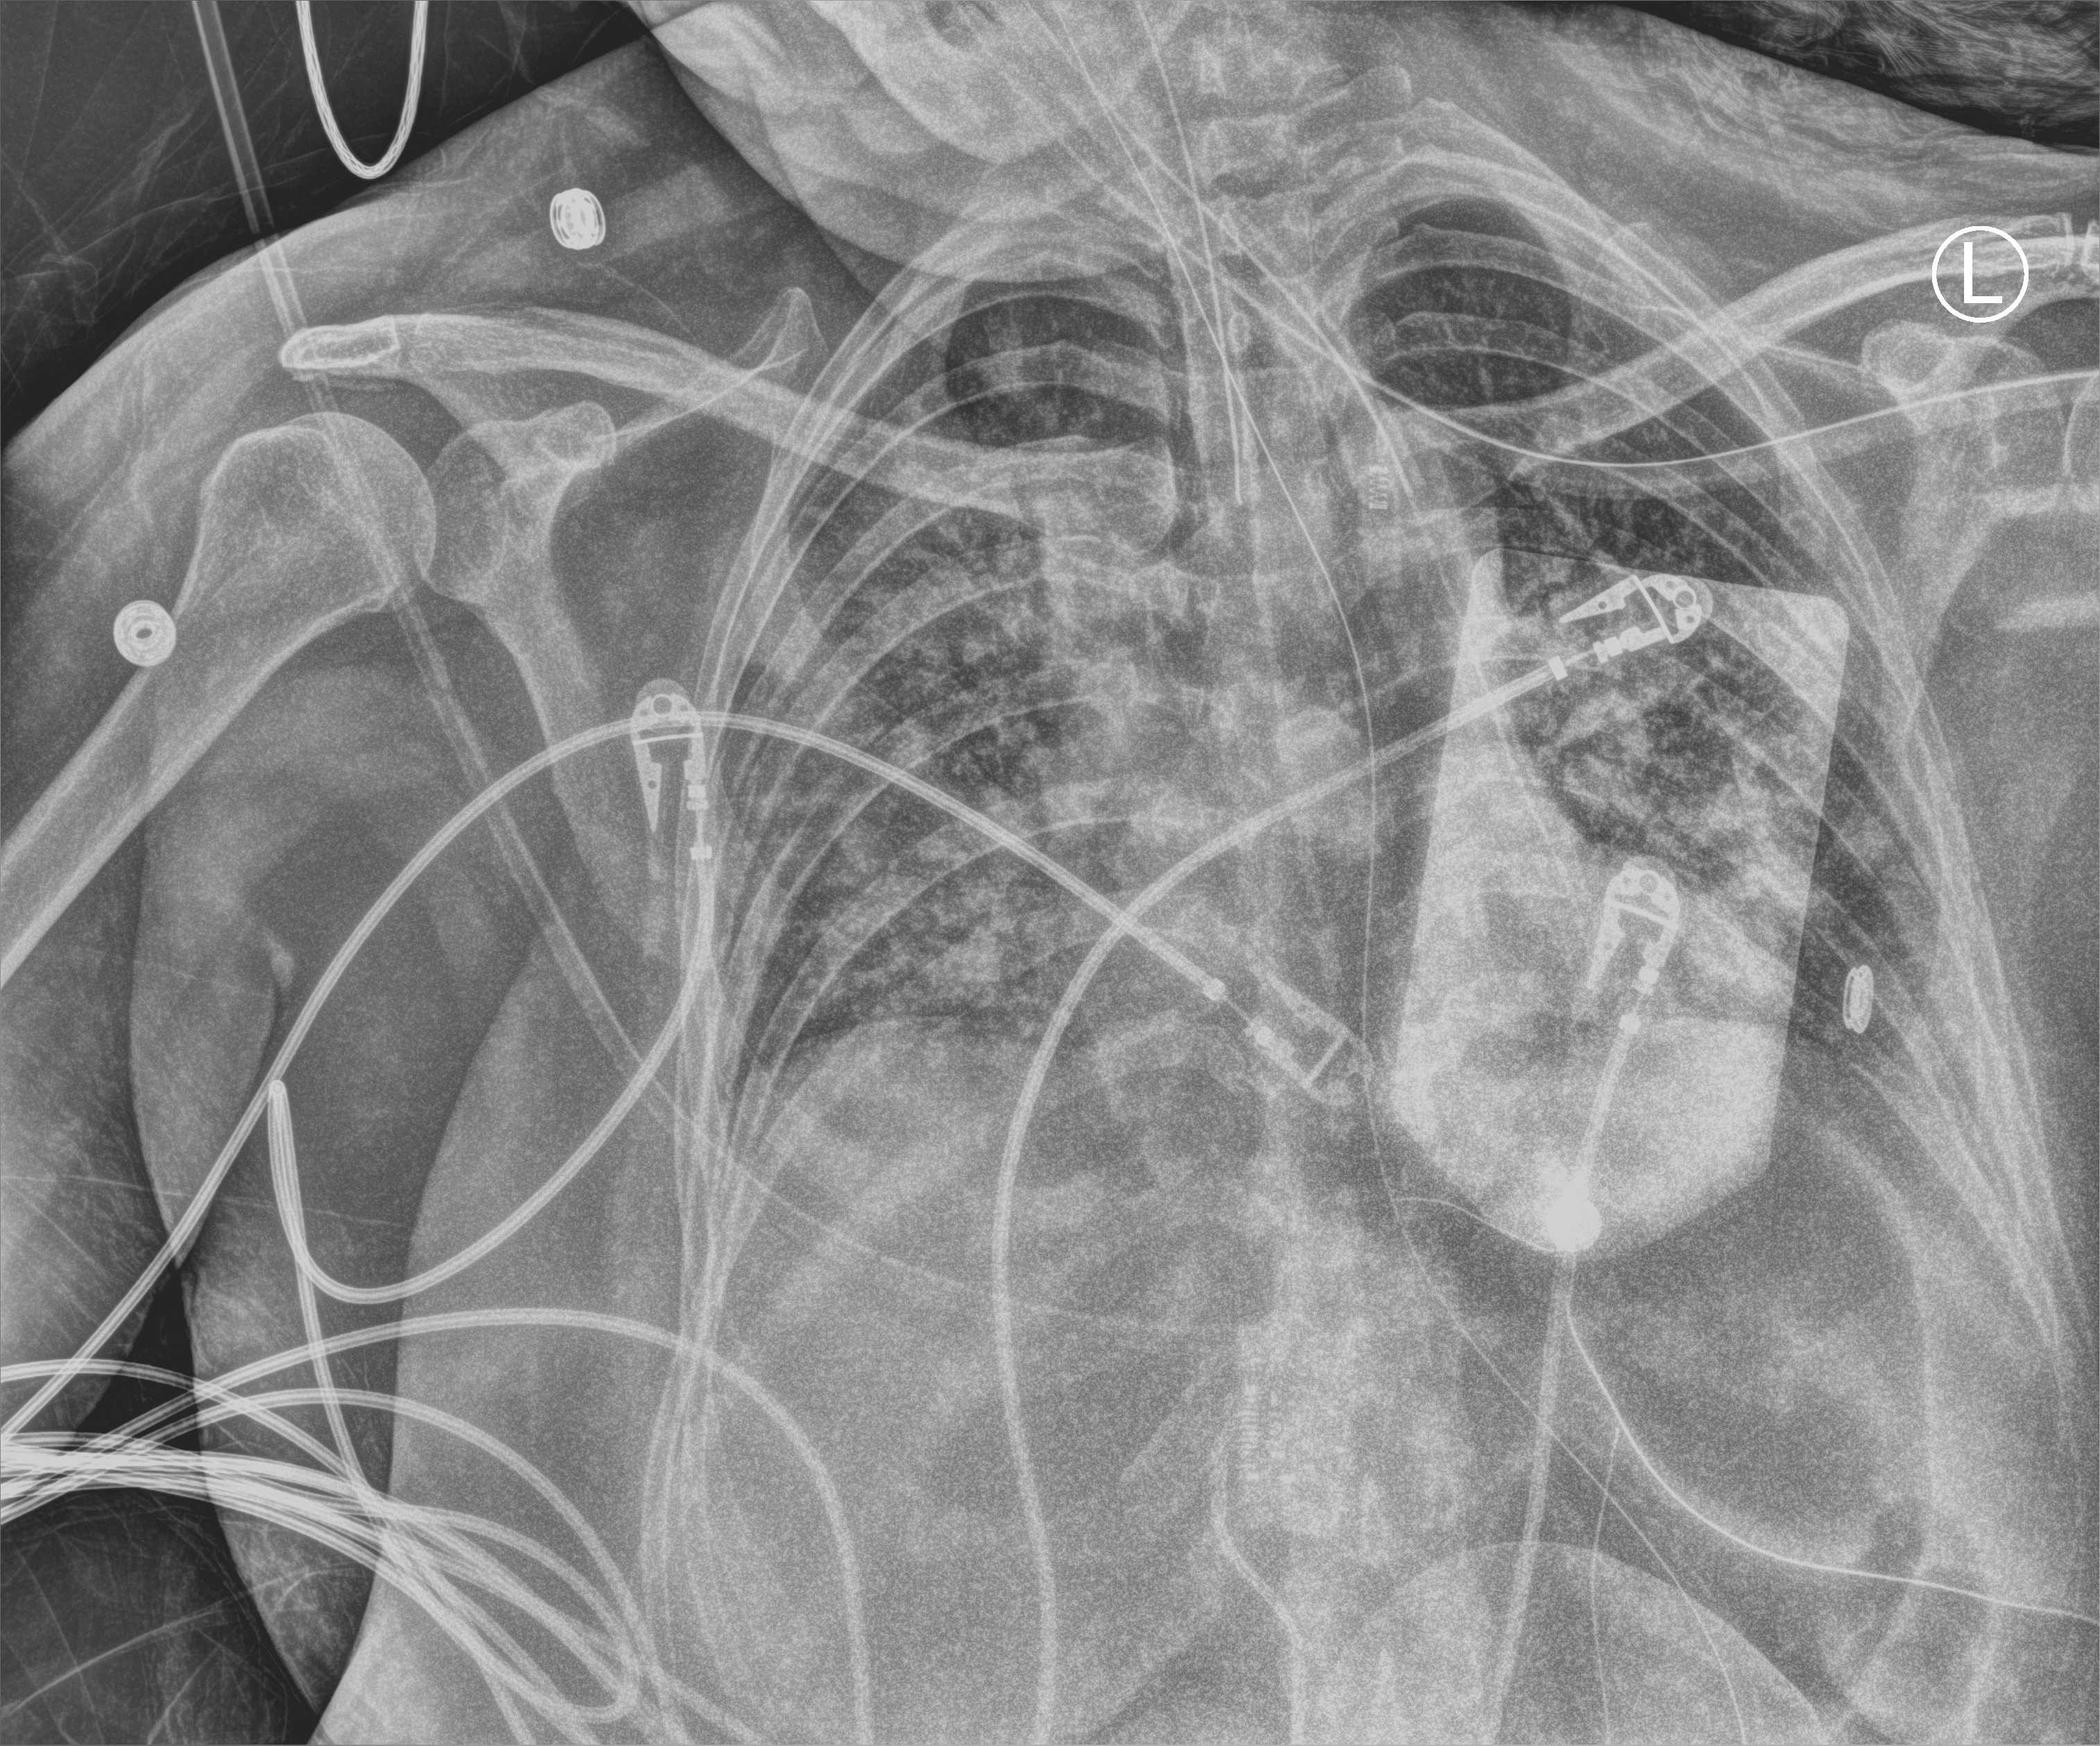
Portable chest radiograph. Female patient hospitalised with COVID-19, age 18–59 years.
From the hospital-stay record, not from the radiograph (when in the stay this image was taken is not recorded): admitted to intensive care during this hospital stay: yes.